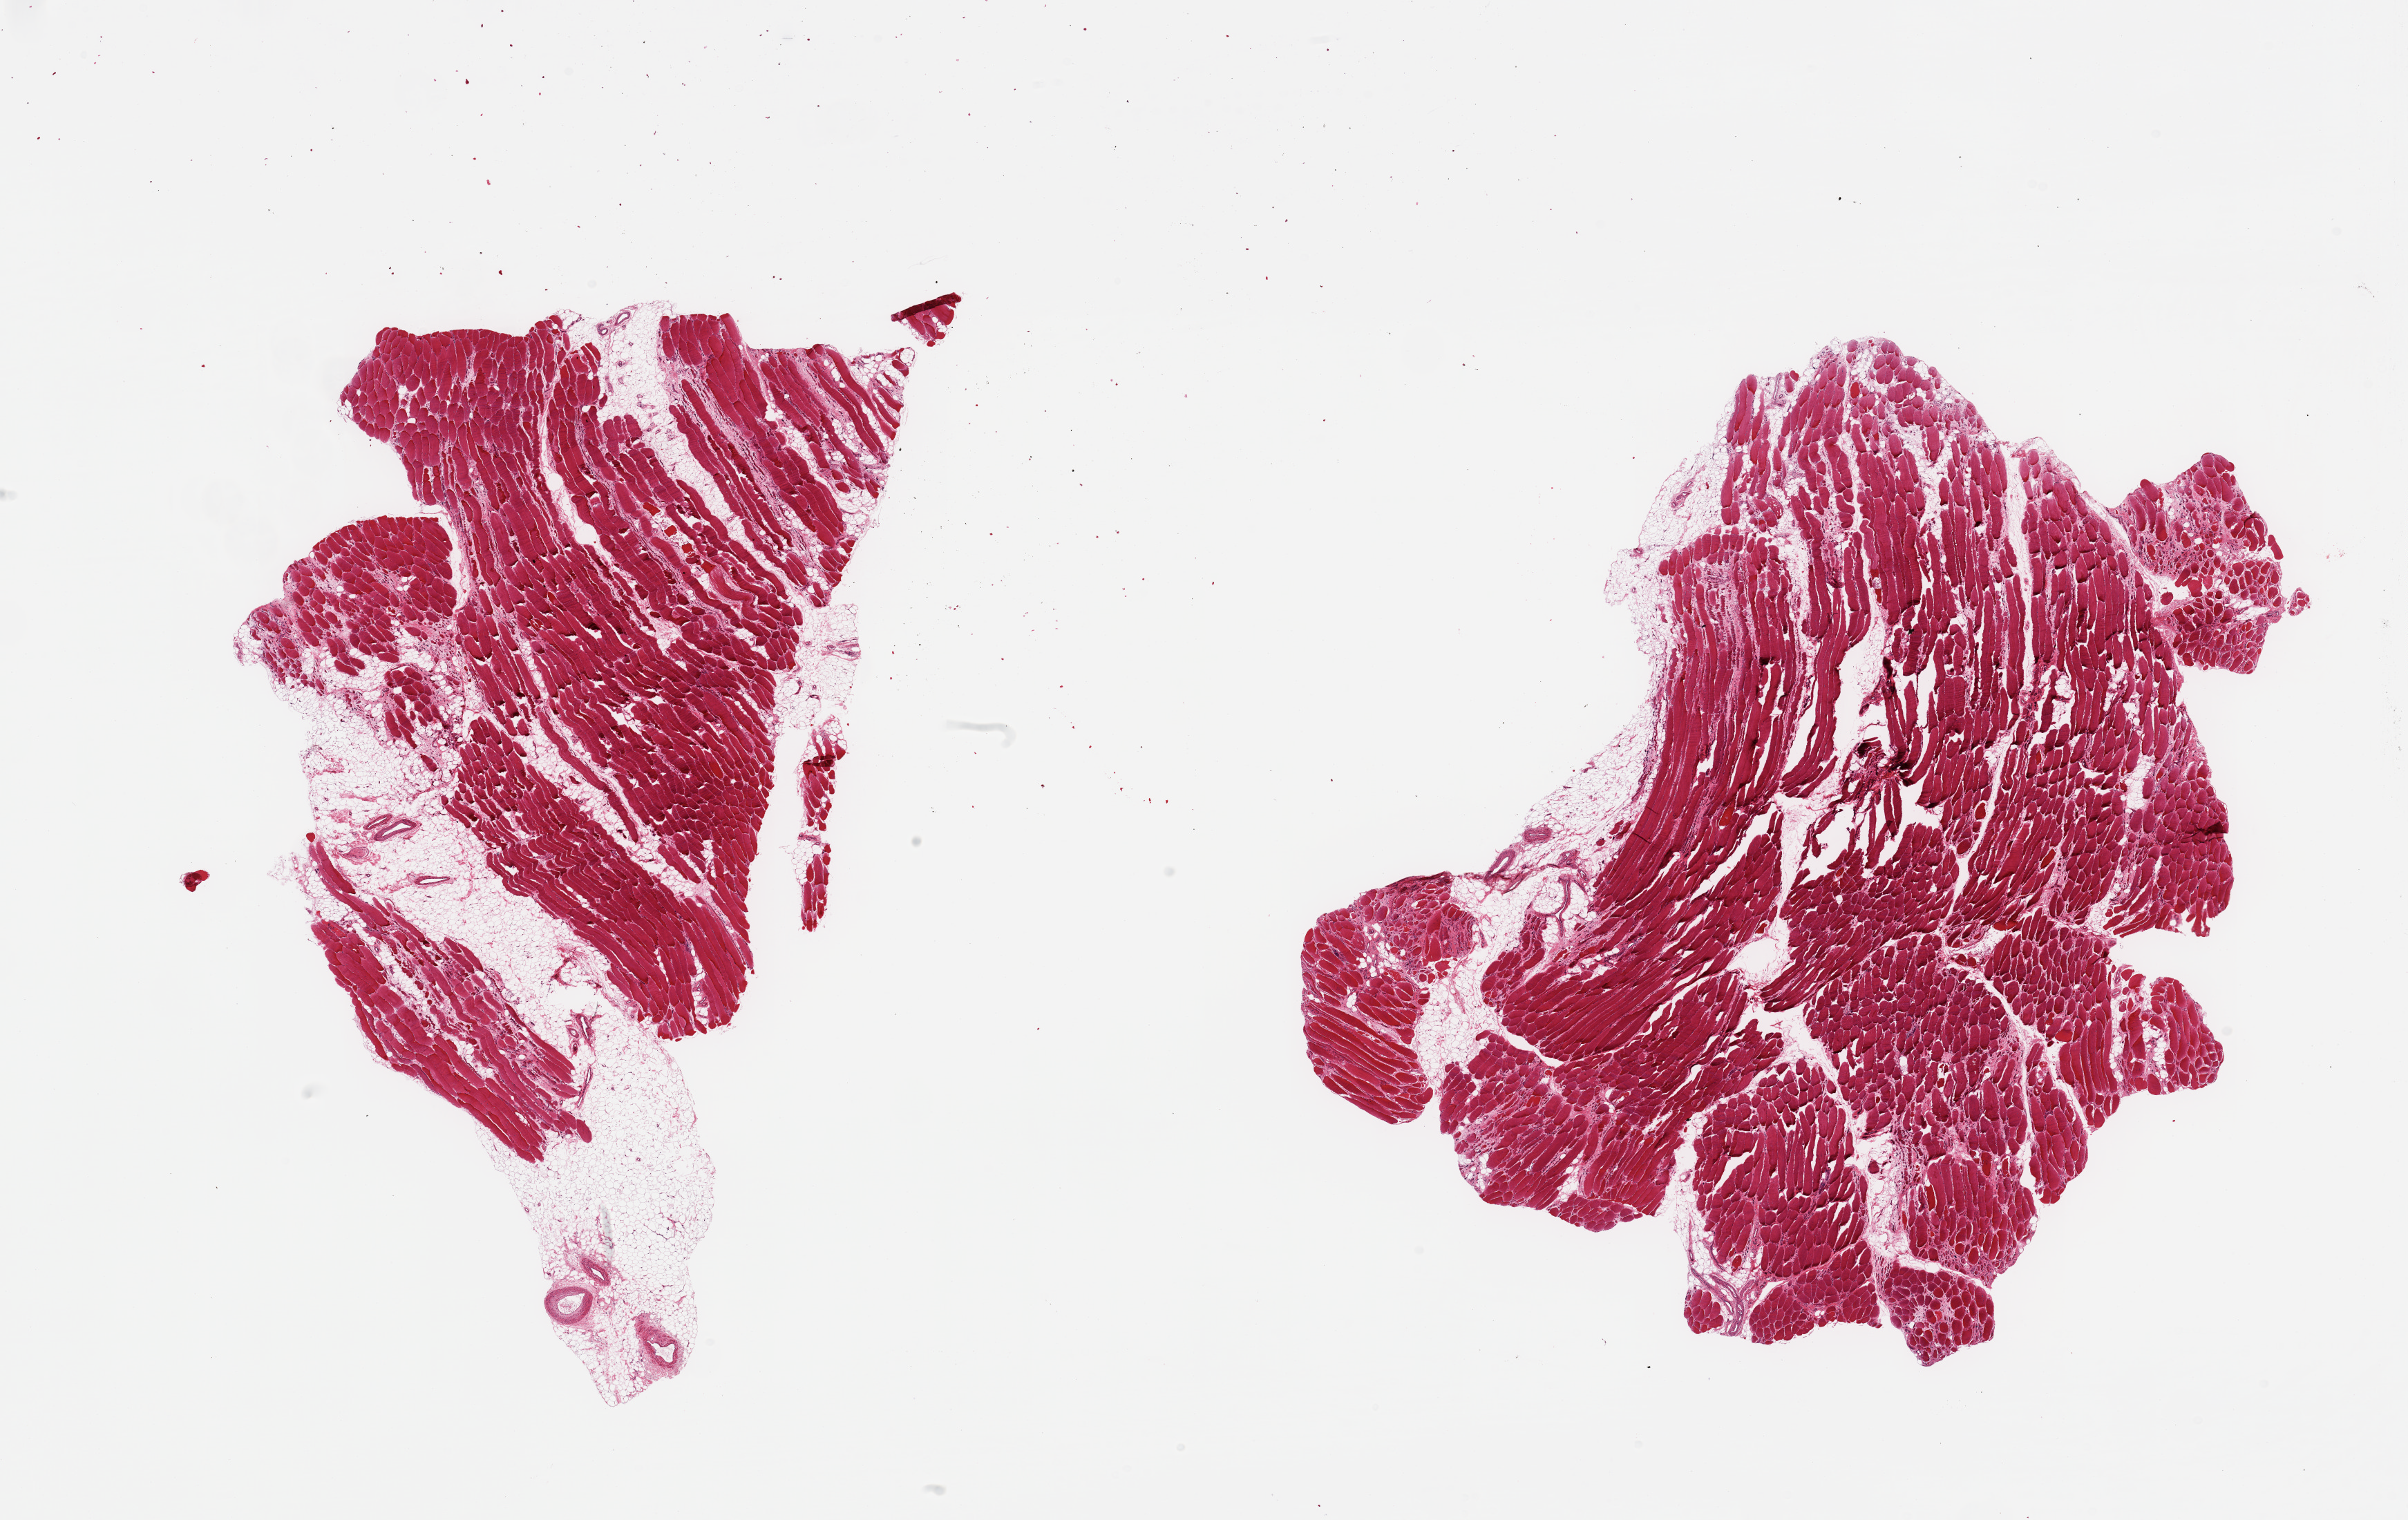
Whole-slide image, H&E stain — whole scanned area (about 27.6 x 17.4 mm) shown as a low-resolution overview, PAXgene-fixed paraffin-embedded (PFPE) section, sampled site (target tissue): skeletal muscle, donor tissue sample.
Review note (as recorded): 2 pieces; focal atrophic fibers; 10% internal fat content.